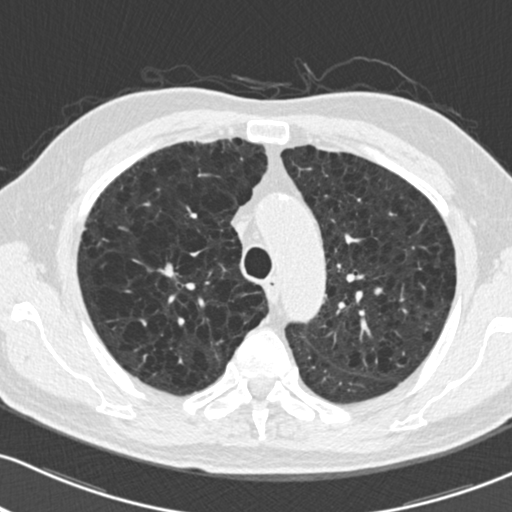
Axial slice from a low-dose chest CT screening exam. Second annual screen. Lung window (W 1500 / L -600 HU). 2 mm slice thickness. Standard (soft-tissue) reconstruction kernel (B30f). Slice 50 of 204 in the series. Male participant, aged 73 years at enrolment.
• Lesion marked by an expert reader, bounding box <151,256,192,288> (left, top, right, bottom; pixels).
• Screening reader's record for this exam (one nodule recorded; not confirmed to be the boxed lesion): non-calcified nodule or mass ≥4 mm, right upper lobe, 10 × 9 mm, smooth margins, soft tissue attenuation, pre-existing on the prior screen: yes; interval growth: yes.
• Official screen result: positive, other.
• Later outcome: lung cancer diagnosed 51 days after this screen — squamous cell carcinoma, NOS, right upper lobe, stage IA (AJCC 6th edition), 10 mm at pathology.